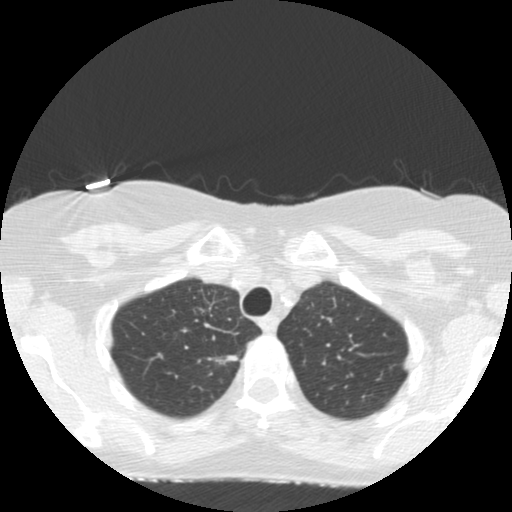
Low-dose screening chest CT, axial slice, baseline screening round, lung window (W 1500 / L -600 HU), 120 kVp, slice 29 of 155 in the series, 512 × 512 image matrix. Female, age 67 years at enrolment. Former smoker at enrolment.
Expert reader's lesion annotation, bounding box (x1, y1, x2, y2) in pixels: (195, 338, 254, 387). Reader record for this screening exam (exam-level; its link to the box is not recorded): non-calcified nodule or mass ≥4 mm, right upper lobe, 16 × 7 mm, poorly defined margins, mixed attenuation.